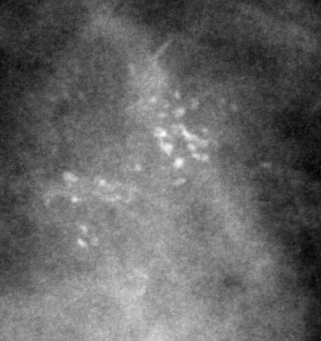
Region of interest cut from a scanned film mammogram (one marked finding), left breast, CC view, BI-RADS breast density category 4 (scale 1–4).
- Finding: calcifications, morphology pleomorphic, distribution clustered; BI-RADS assessment category 4; subtlety rating 5 on a 1 (subtle) to 5 (obvious) scale; pathology (as recorded): malignant.